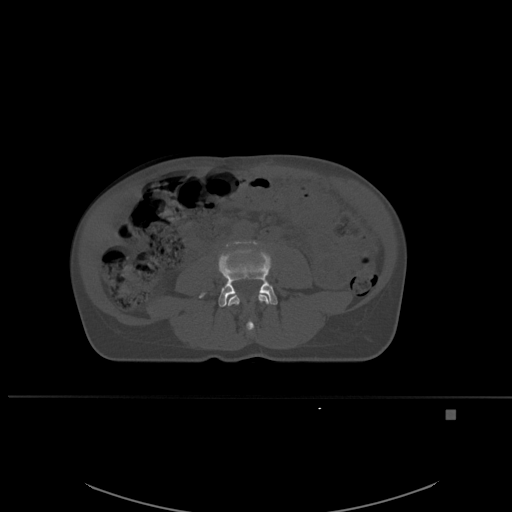
CT including the spine, one axial slice. Slice 200 of 537 in the series (ordered by position). Bone window (W 1800 / L 400 HU). 512 × 512 image matrix, field of view 440 × 440 mm. Female patient, age 45 years. From the clinical record (not read from this slice): primary cancer: lung.
Structures marked on this image (semi-automatically segmented with operator editing):
- L3 vertebra: bounding box [x1, y1, x2, y2] px = [228, 293, 271, 332]
- L4 vertebra: [199, 240, 278, 307]